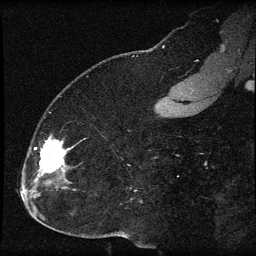
Breast MRI (dynamic contrast-enhanced), one sagittal slice. Slice 24 of 60 in the series (ordered by position). Dynamic contrast-enhanced series, image 2 of 3 at this slice position (ordered by acquisition). 1.5 T. TE 4.2 ms, TR 8.2 ms. 2 mm slice thickness. 256 × 256 image matrix, field of view 180 × 180 mm. Female patient, age 32 years.
Structures marked on this image (semi-automatic segmentation, software-assisted and operator-edited):
- analysis volume of interest (the breast-tissue region the enhancement analysis was run in; not a lesion): bounding box [x1, y1, x2, y2] px = [31, 136, 71, 184]
- tumour enhancement mask (voxels above the 70 % enhancement threshold inside the analysis volume of interest): [35, 136, 69, 182]